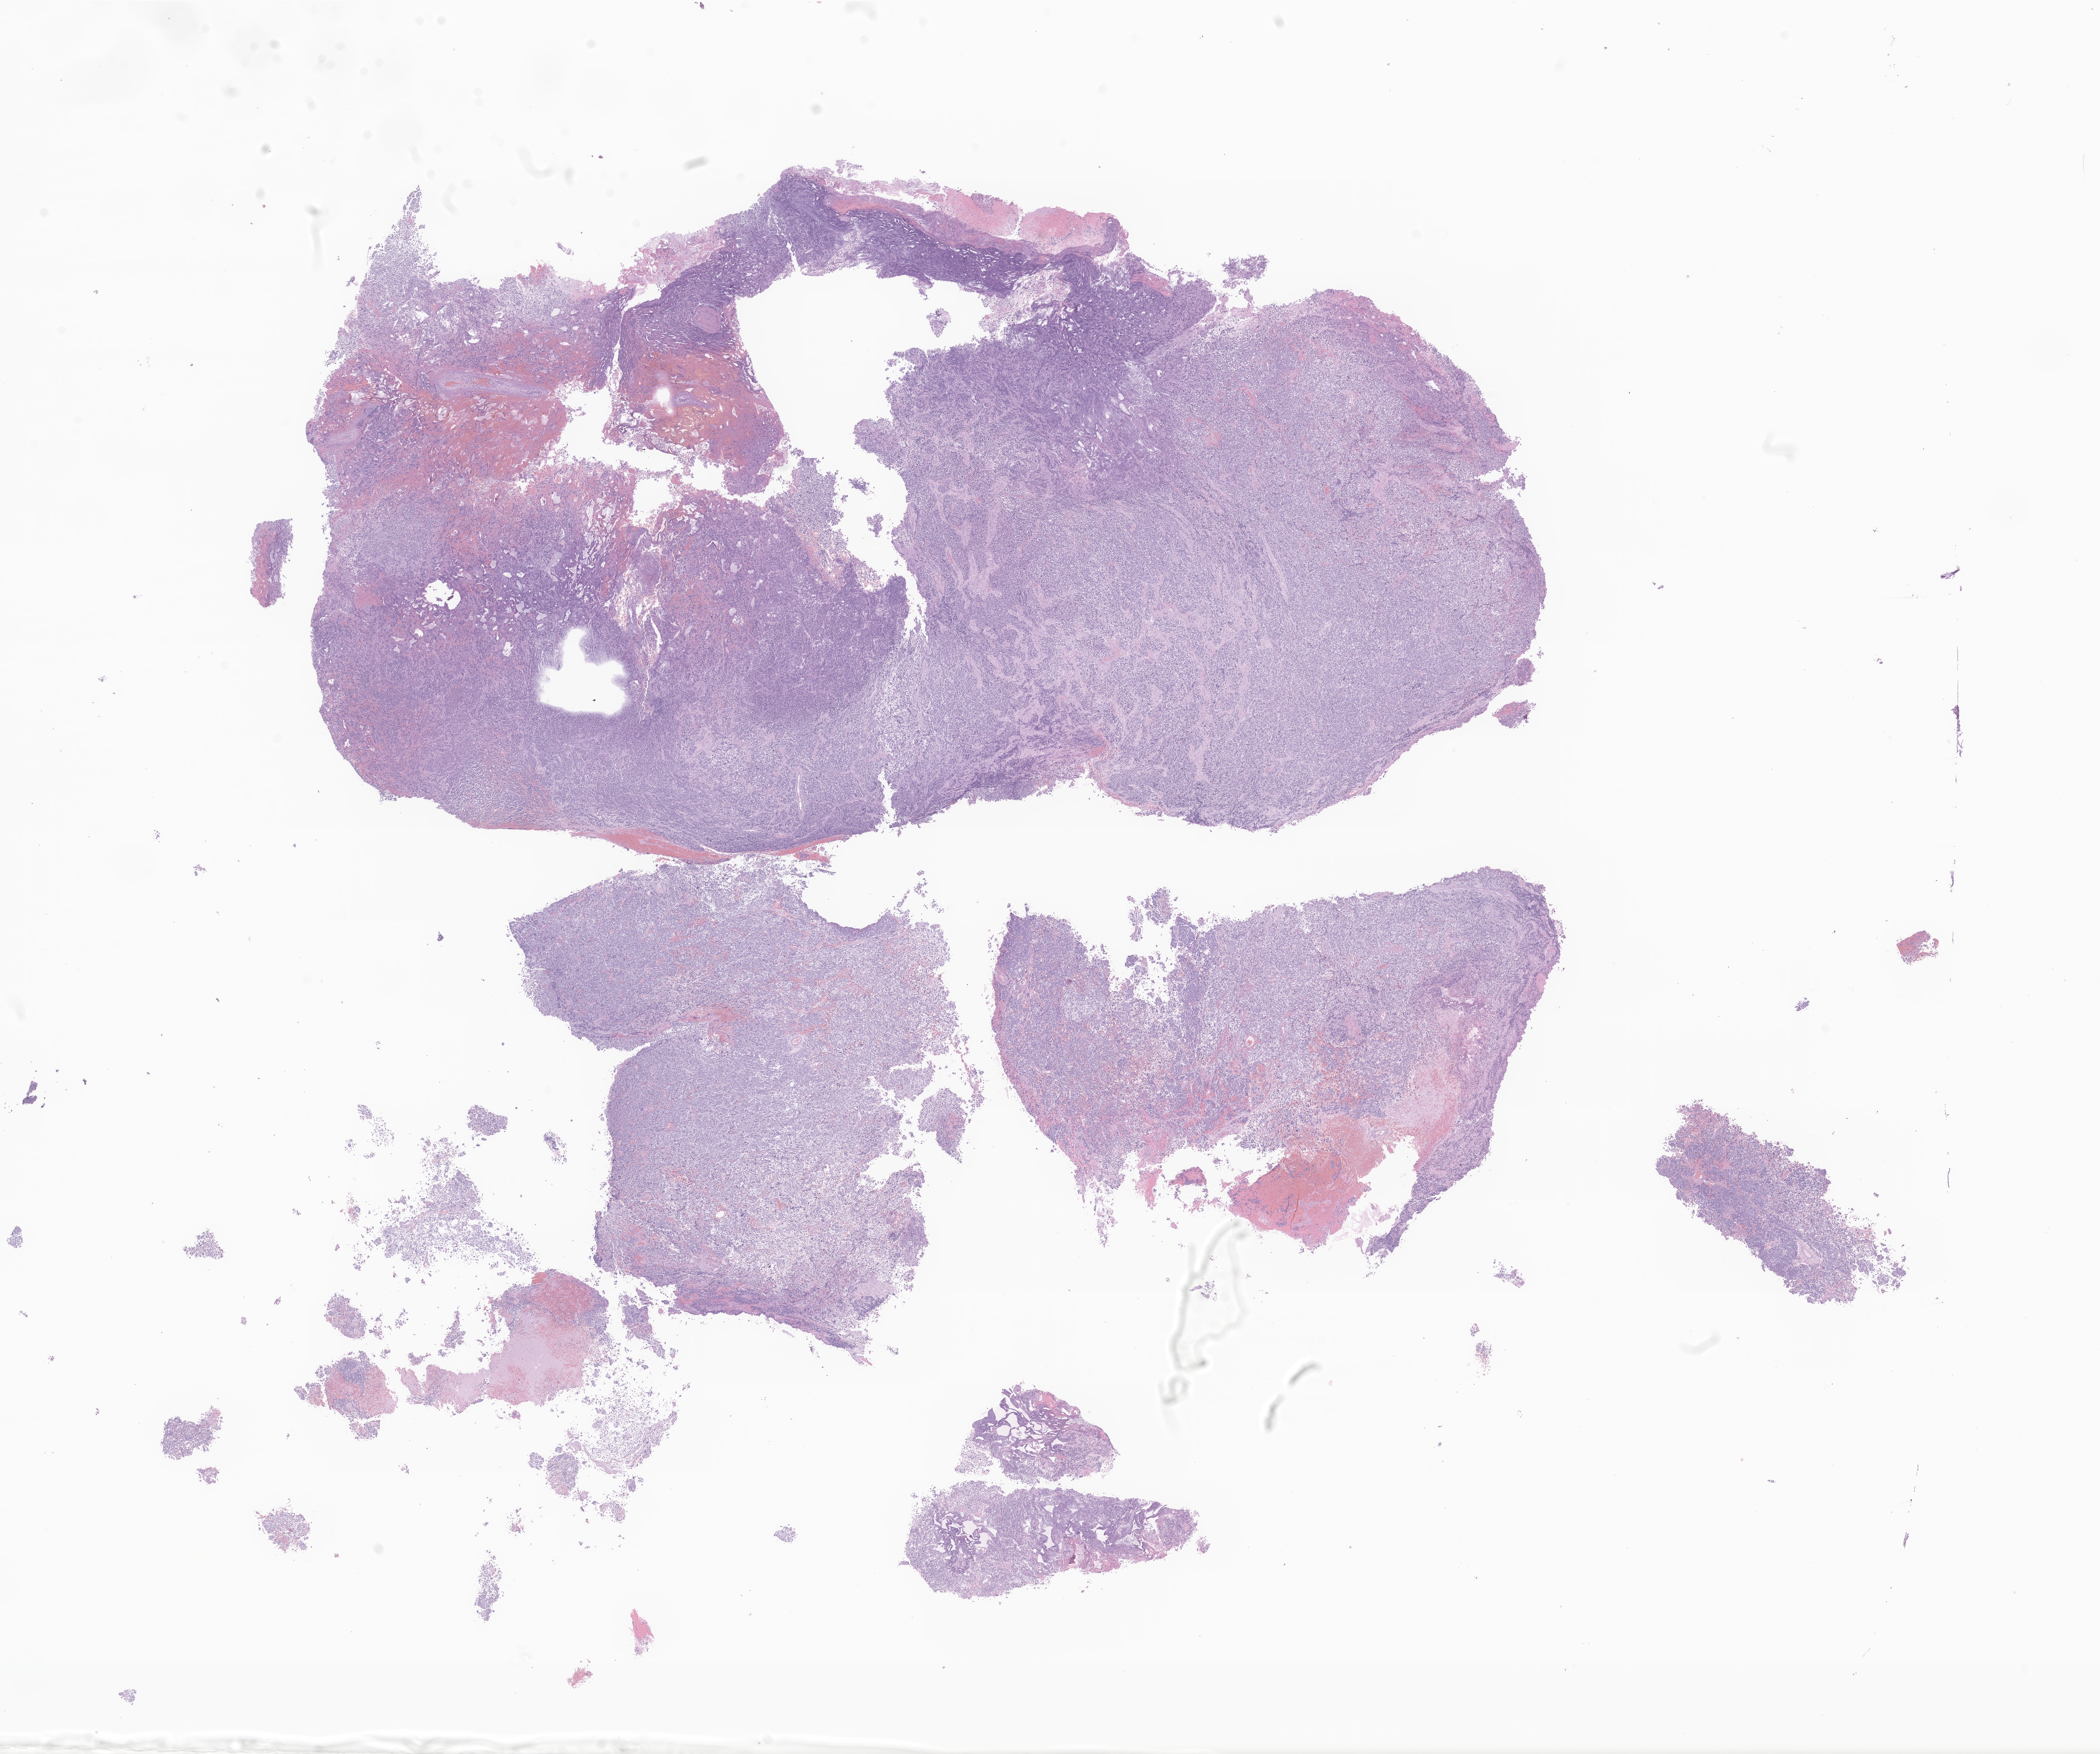
Digitized haematoxylin and eosin-stained section of tumor tissue from the brain — low-resolution overview of the scanned area, about 24.2 x 20.2 mm. Formalin-fixed, paraffin-embedded (FFPE) tissue. Female patient, age 146 months (12 years 2 months).
Diagnosis: Medulloblastoma, NOS.